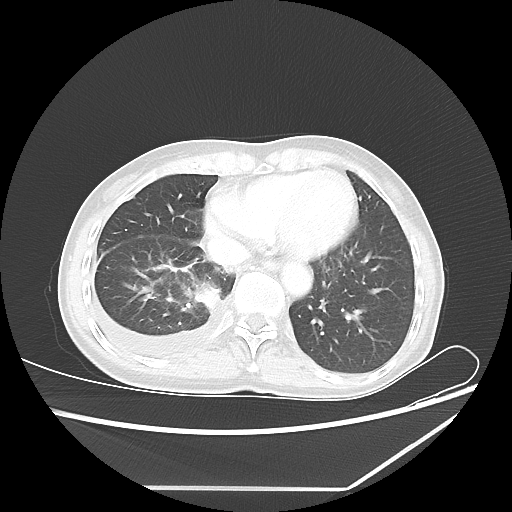
Chest CT, one axial slice; position 19 of 60 along the scan axis; reconstruction kernel LUNG; 80 kVp; lung window (W 1500 / L -600 HU); 5 mm slice thickness; 512 × 512 image matrix, field of view 364 × 364 mm. Patient: female, 59 years. From the clinical record (not read from this slice): clinical TNM (as recorded): T1c N1 M1.
Outlined on this slice (bounding box drawn by a radiologist):
- lung tumour (recorded histology: adenocarcinoma): bounding box [x1, y1, x2, y2] px = [191, 281, 223, 314]